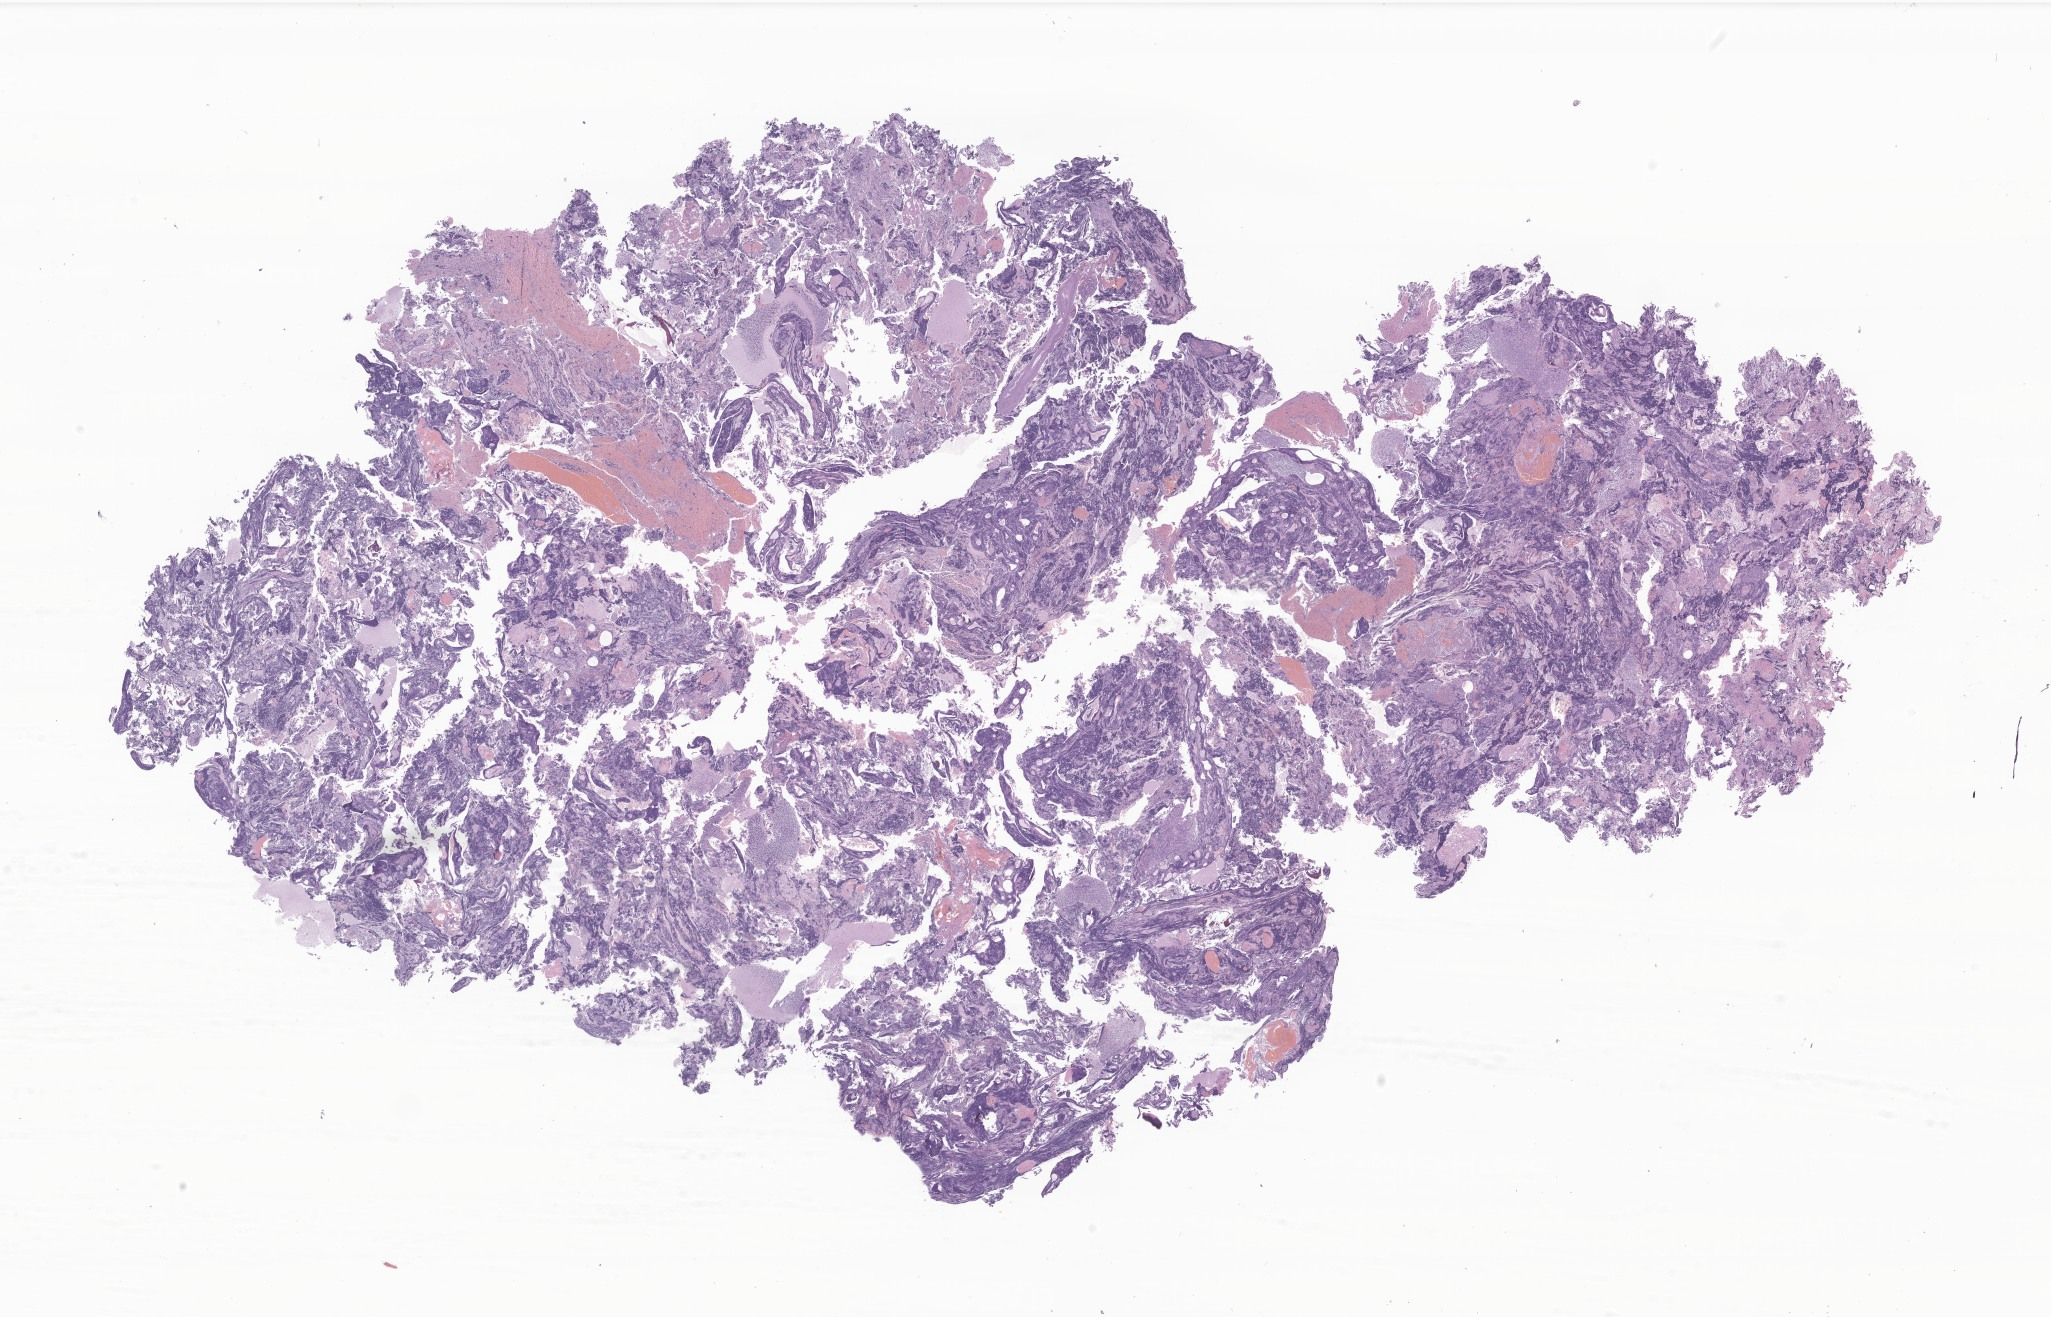
H&E whole-slide image of tumor tissue from the cerebellum — low-resolution overview of the scanned area, about 34.6 x 22.2 mm; FFPE section. Male patient, age 133 months (11 years 1 month).
Diagnosis (ICD-O-3 morphology term): Medulloblastoma, NOS.